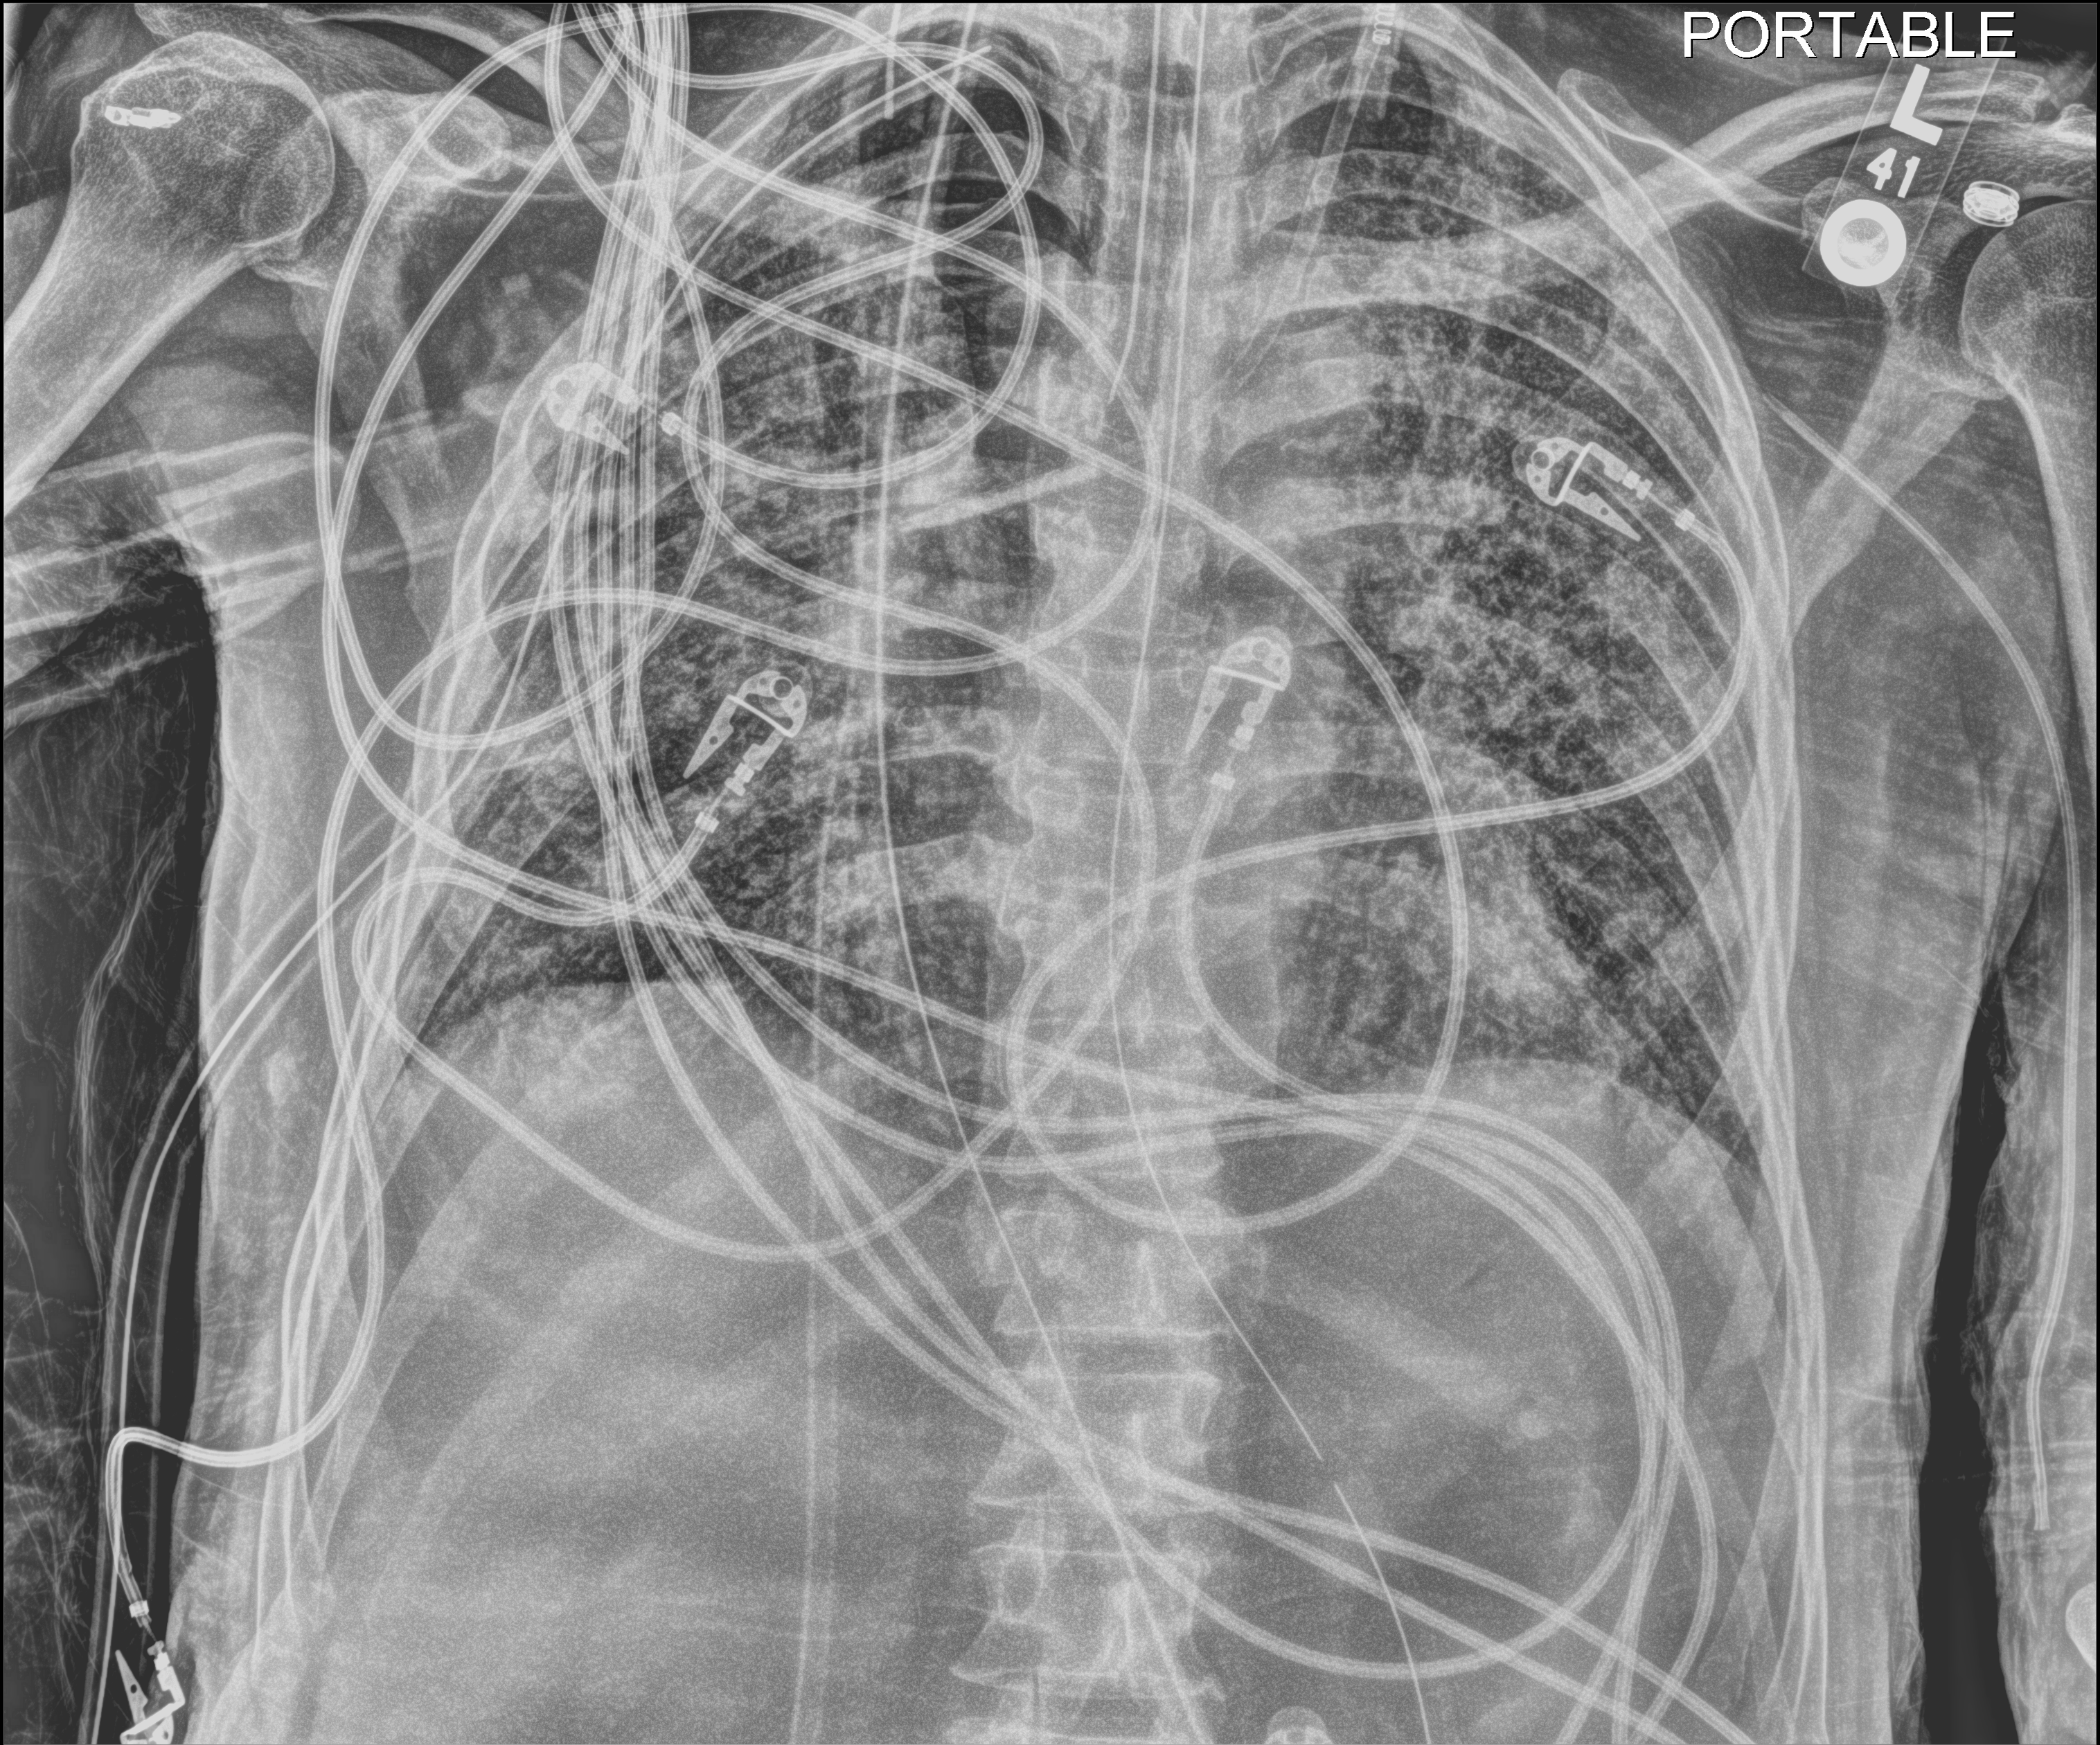
Chest X-ray. Patient hospitalised with COVID-19; male, aged 60–74 years.
From the hospital-stay record, not from the radiograph (when in the stay this image was taken is not recorded): admitted to intensive care during this hospital stay: yes; mechanically ventilated during this hospital stay: yes; diabetes (admission record): no.